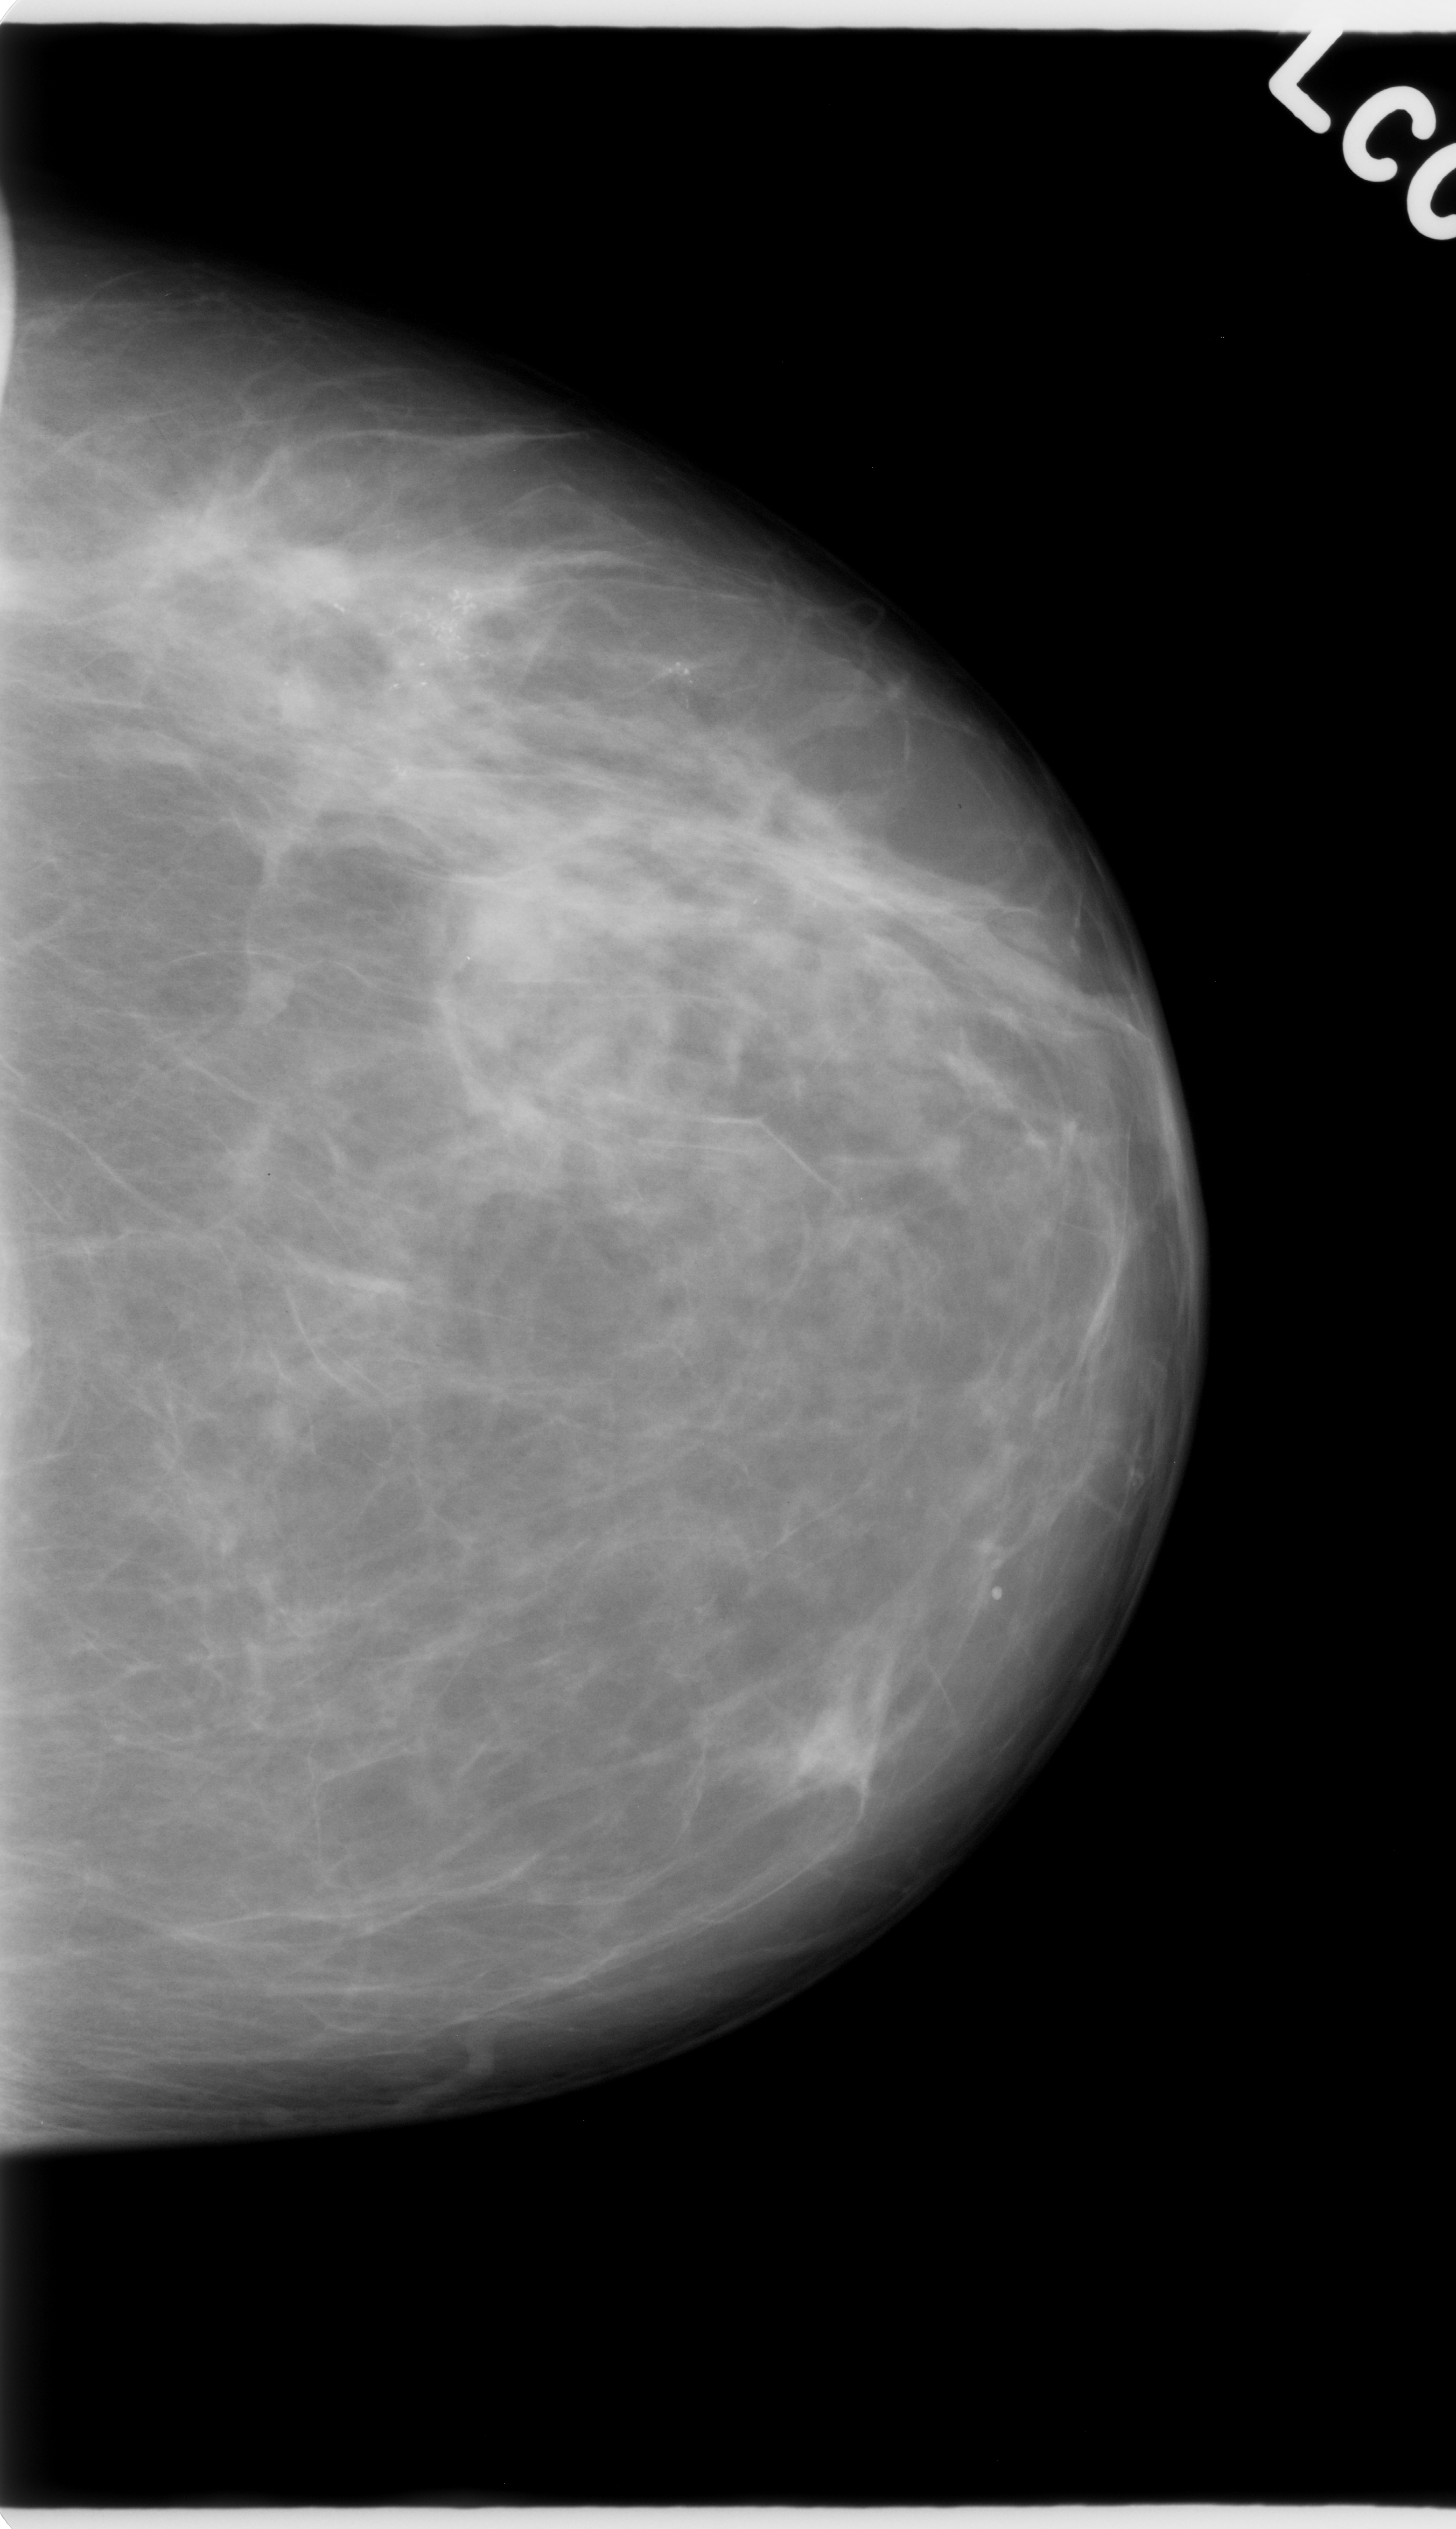
Scanned film-screen mammogram; left breast; CC view; BI-RADS breast density category 2 (scale 1–4).
Radiologist-marked abnormalities on this image: Finding 1 of 2: calcifications, morphology pleomorphic, distribution clustered; BI-RADS assessment category 5; pathology (as recorded): malignant. Finding 2 of 2: calcifications, morphology pleomorphic, distribution clustered; BI-RADS assessment category 5; pathology (as recorded): malignant.